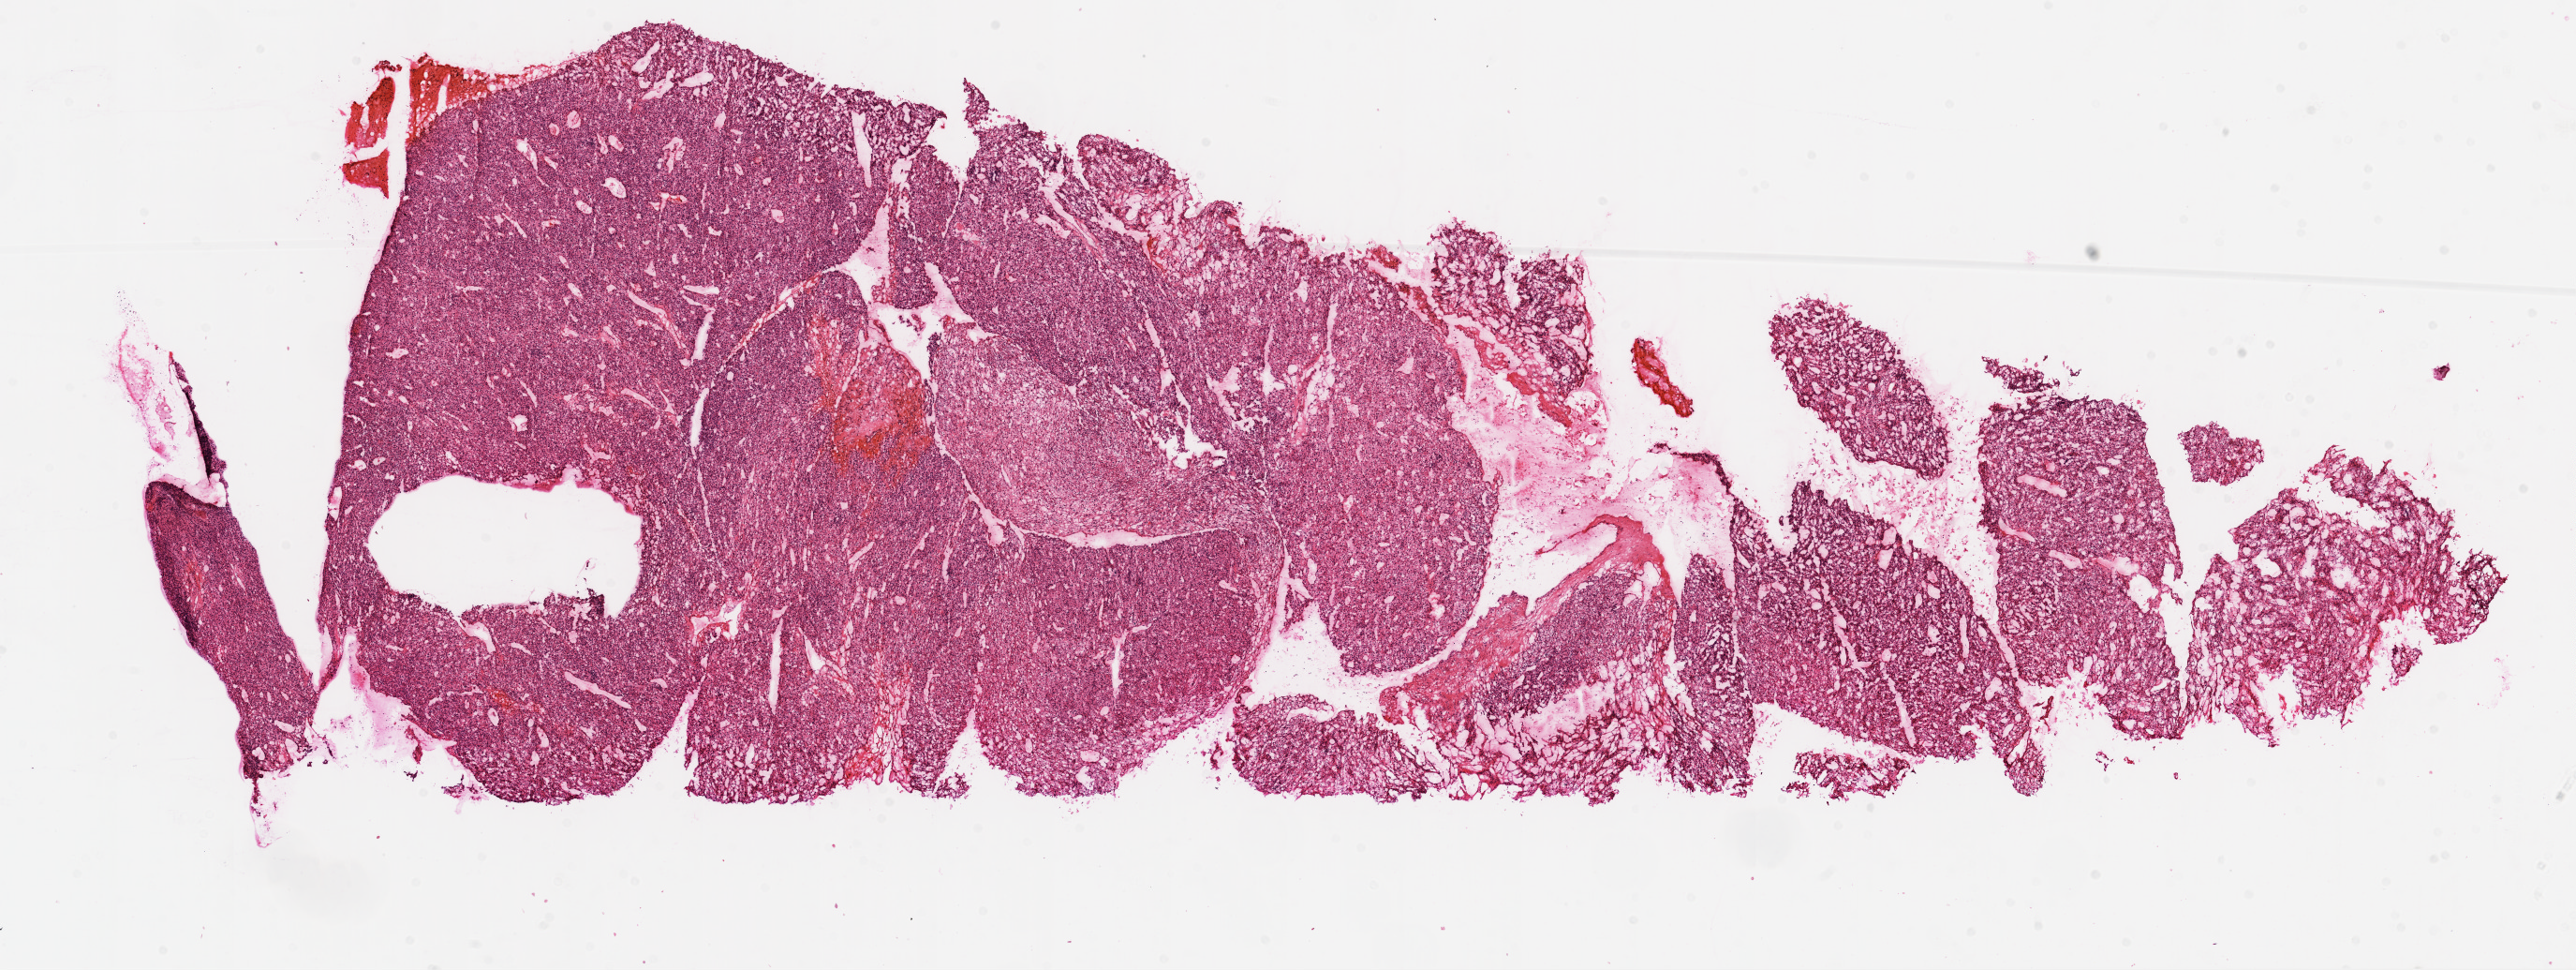
Whole-slide histology image, H&E, low-resolution overview of the scanned area, about 22.1 x 8.3 mm (acquisition: 20x scan); frozen section from the top of the tissue portion; primary tumour sample from the kidney. Female patient; age at initial diagnosis 73 years. Composition of this section per pathologist review: tumour cells 95%, tumour nuclei 90%.
Histologic diagnosis: Clear cell adenocarcinoma, NOS.